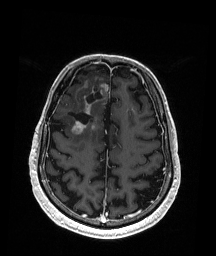
Brain MRI from a brain-tumour surgery series, one axial slice. Slice 59 of 192 in the series (ordered by position). T1-weighted post-contrast. 216 × 256 image matrix, field of view 211 × 250 mm. From the clinical record (not read from this slice): histopathology: Astrocytoma; WHO grade: 3; IDH mutation: yes; tumour location: Right Frontal.
Outlined on this slice (expert manual segmentation):
- previous resection cavity: bounding box (x1, y1, x2, y2) in pixels: (68, 87, 102, 124)
- tumour: (71, 83, 109, 137)